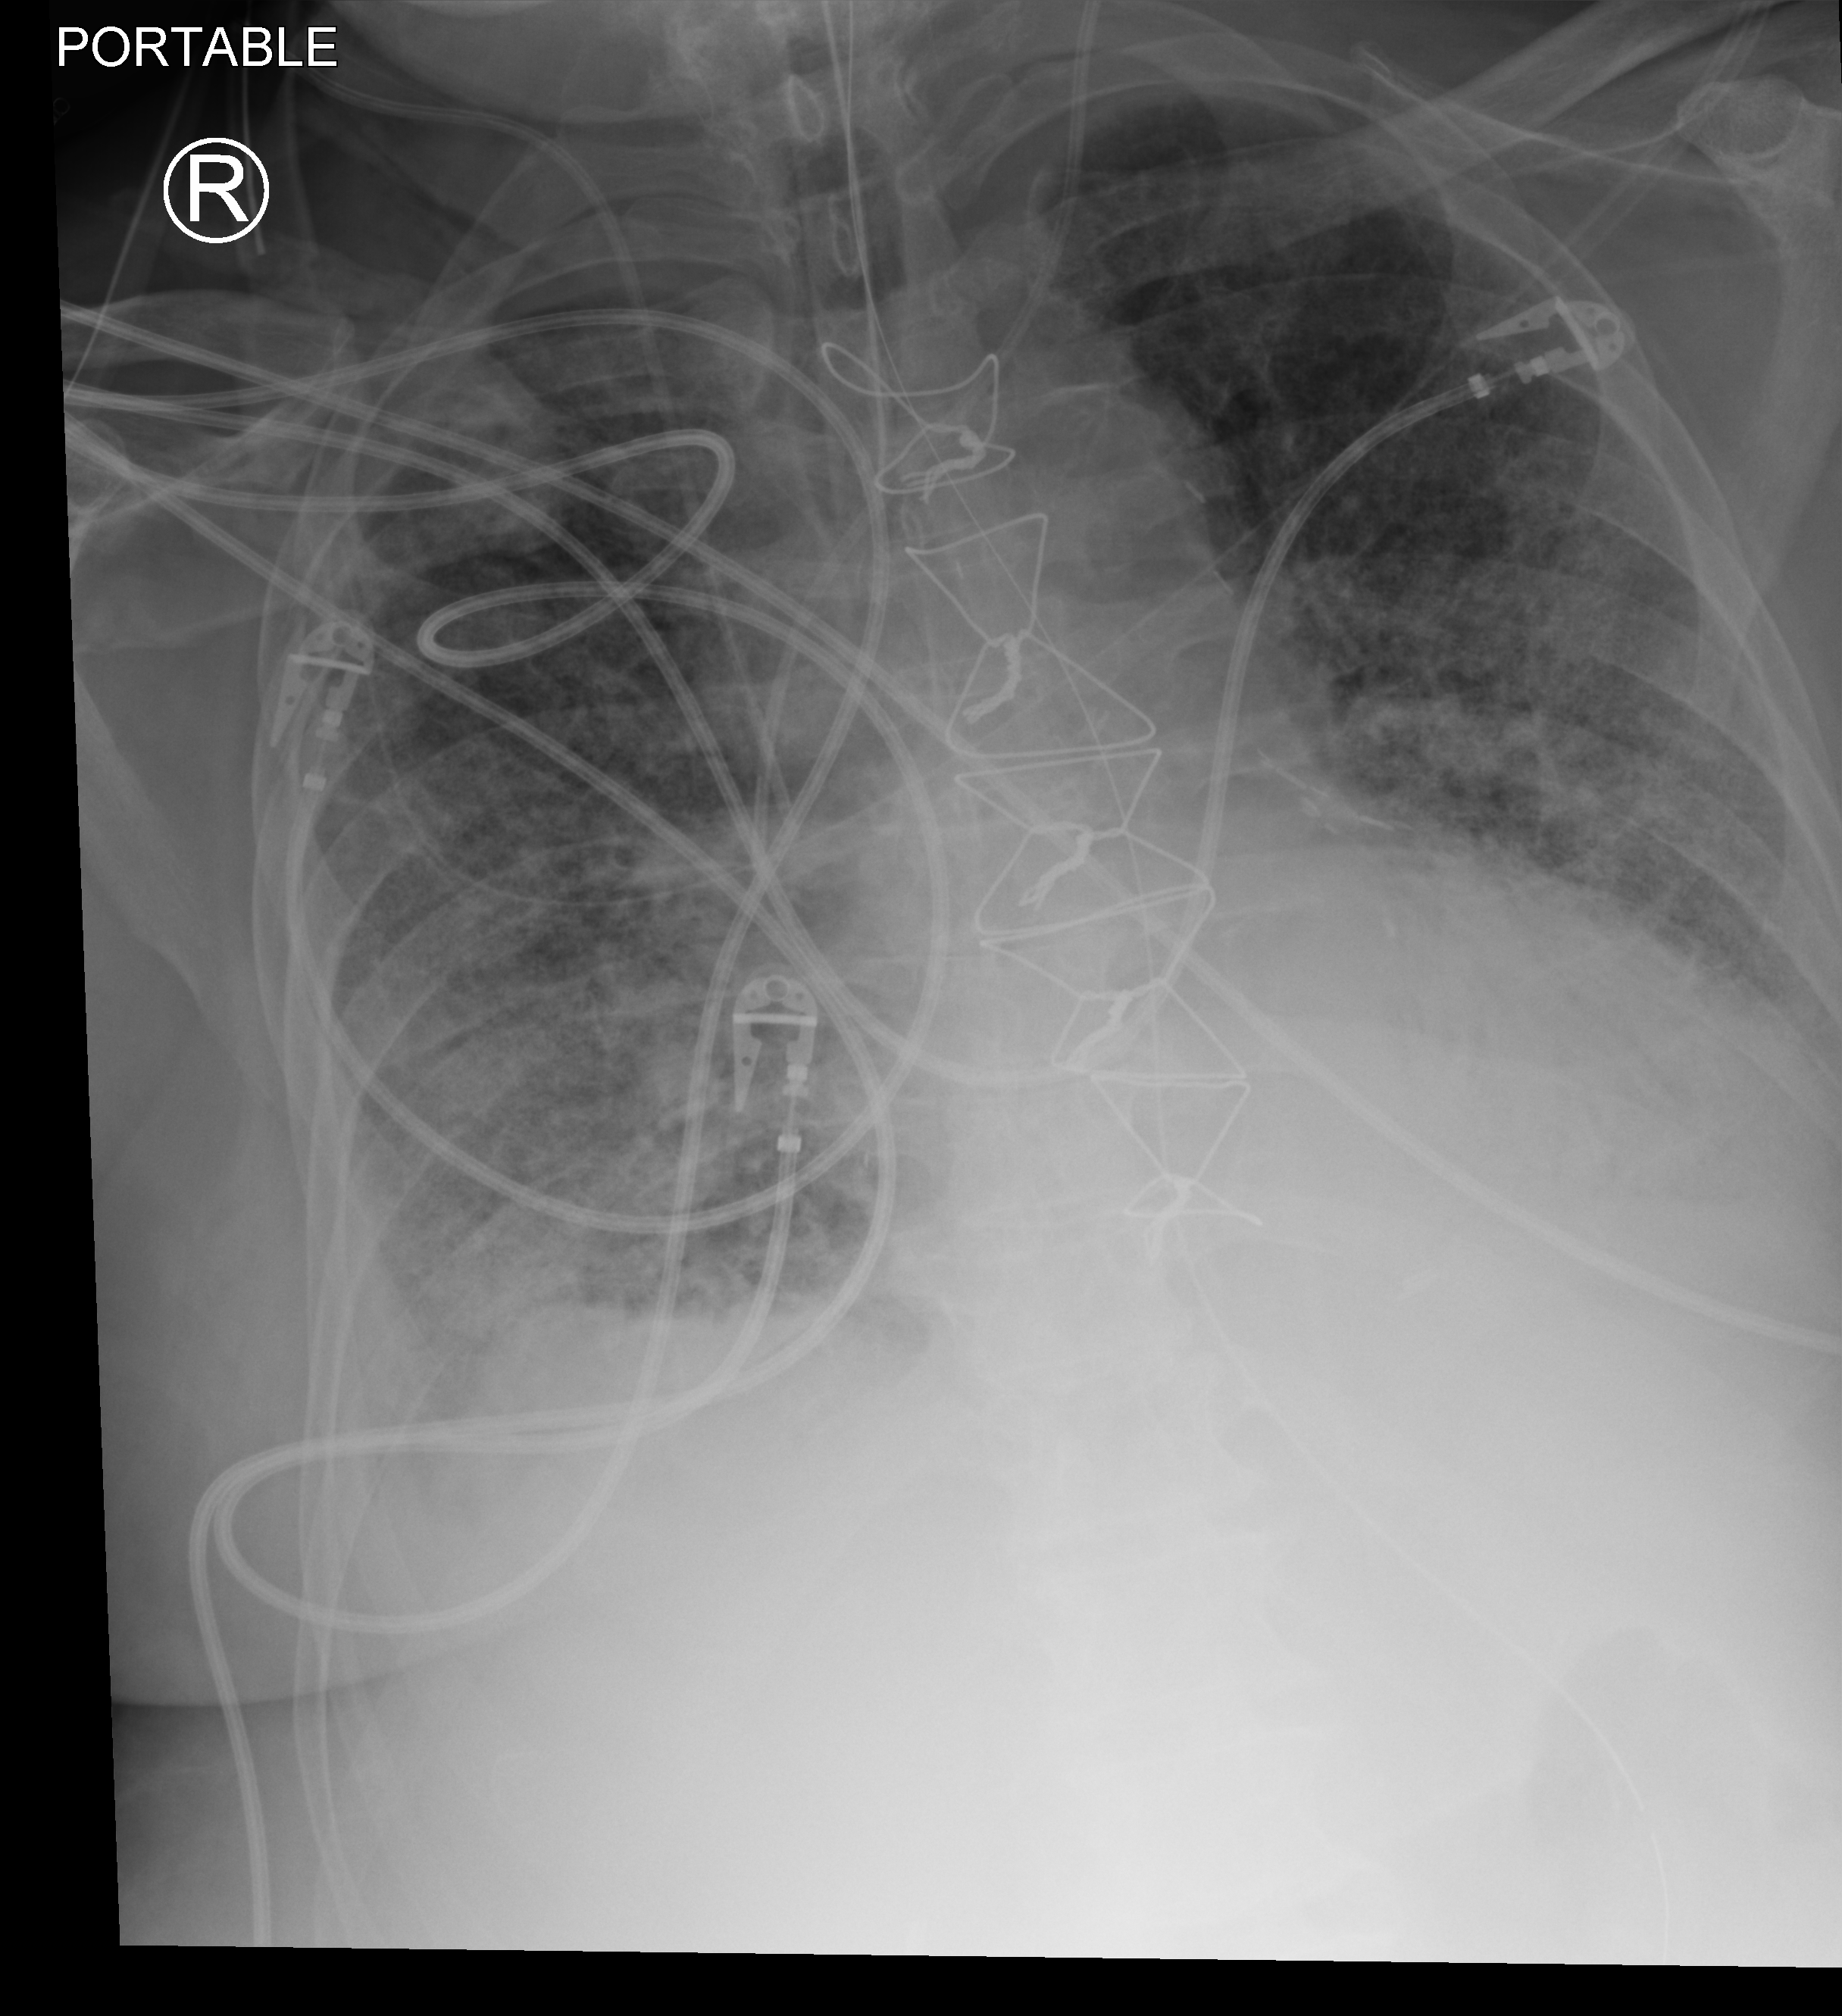
Bedside chest radiograph (computed radiography); anteroposterior (AP) projection. Male patient hospitalised with COVID-19, age 75–90 years.
Hospital-stay facts (about this admission, not read from this image; timing relative to this image not recorded): other chronic lung disease (admission record): yes; admitted to intensive care during this hospital stay: yes; mechanically ventilated during this hospital stay: yes.